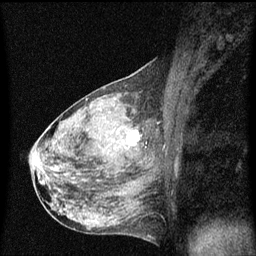
Breast MRI (dynamic contrast-enhanced), one sagittal slice; dynamic contrast-enhanced series, image 2 of 3 at this slice position (ordered by acquisition); 1.5 T; TE 4.2 ms, TR 8 ms; 2 mm slice thickness; 256 × 256 image matrix, field of view 200 × 200 mm. Patient: female, 50 years.
Structures marked on this image (semi-automatically segmented with operator editing):
- analysis volume of interest (the breast-tissue region the enhancement analysis was run in; not a lesion): bounding box <106,118,148,159> (left, top, right, bottom; pixels)
- tumour enhancement mask (voxels above the 70 % enhancement threshold inside the analysis volume of interest): <128,130,140,147>